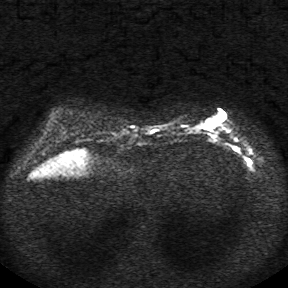
Breast MRI, one axial slice. Position 7 of 34 along the scan axis. Diffusion-weighted series; image 2 of 4 stored at this slice position (different b-values; order by instance number). 1.5 T. 5 mm slice thickness. 288 × 288 image matrix, field of view 340 × 340 mm. Female patient.
Annotated regions visible in this slice (outlined manually by an expert reader):
- tumour on diffusion-weighted imaging: bounding box <195,122,211,128> (left, top, right, bottom; pixels)